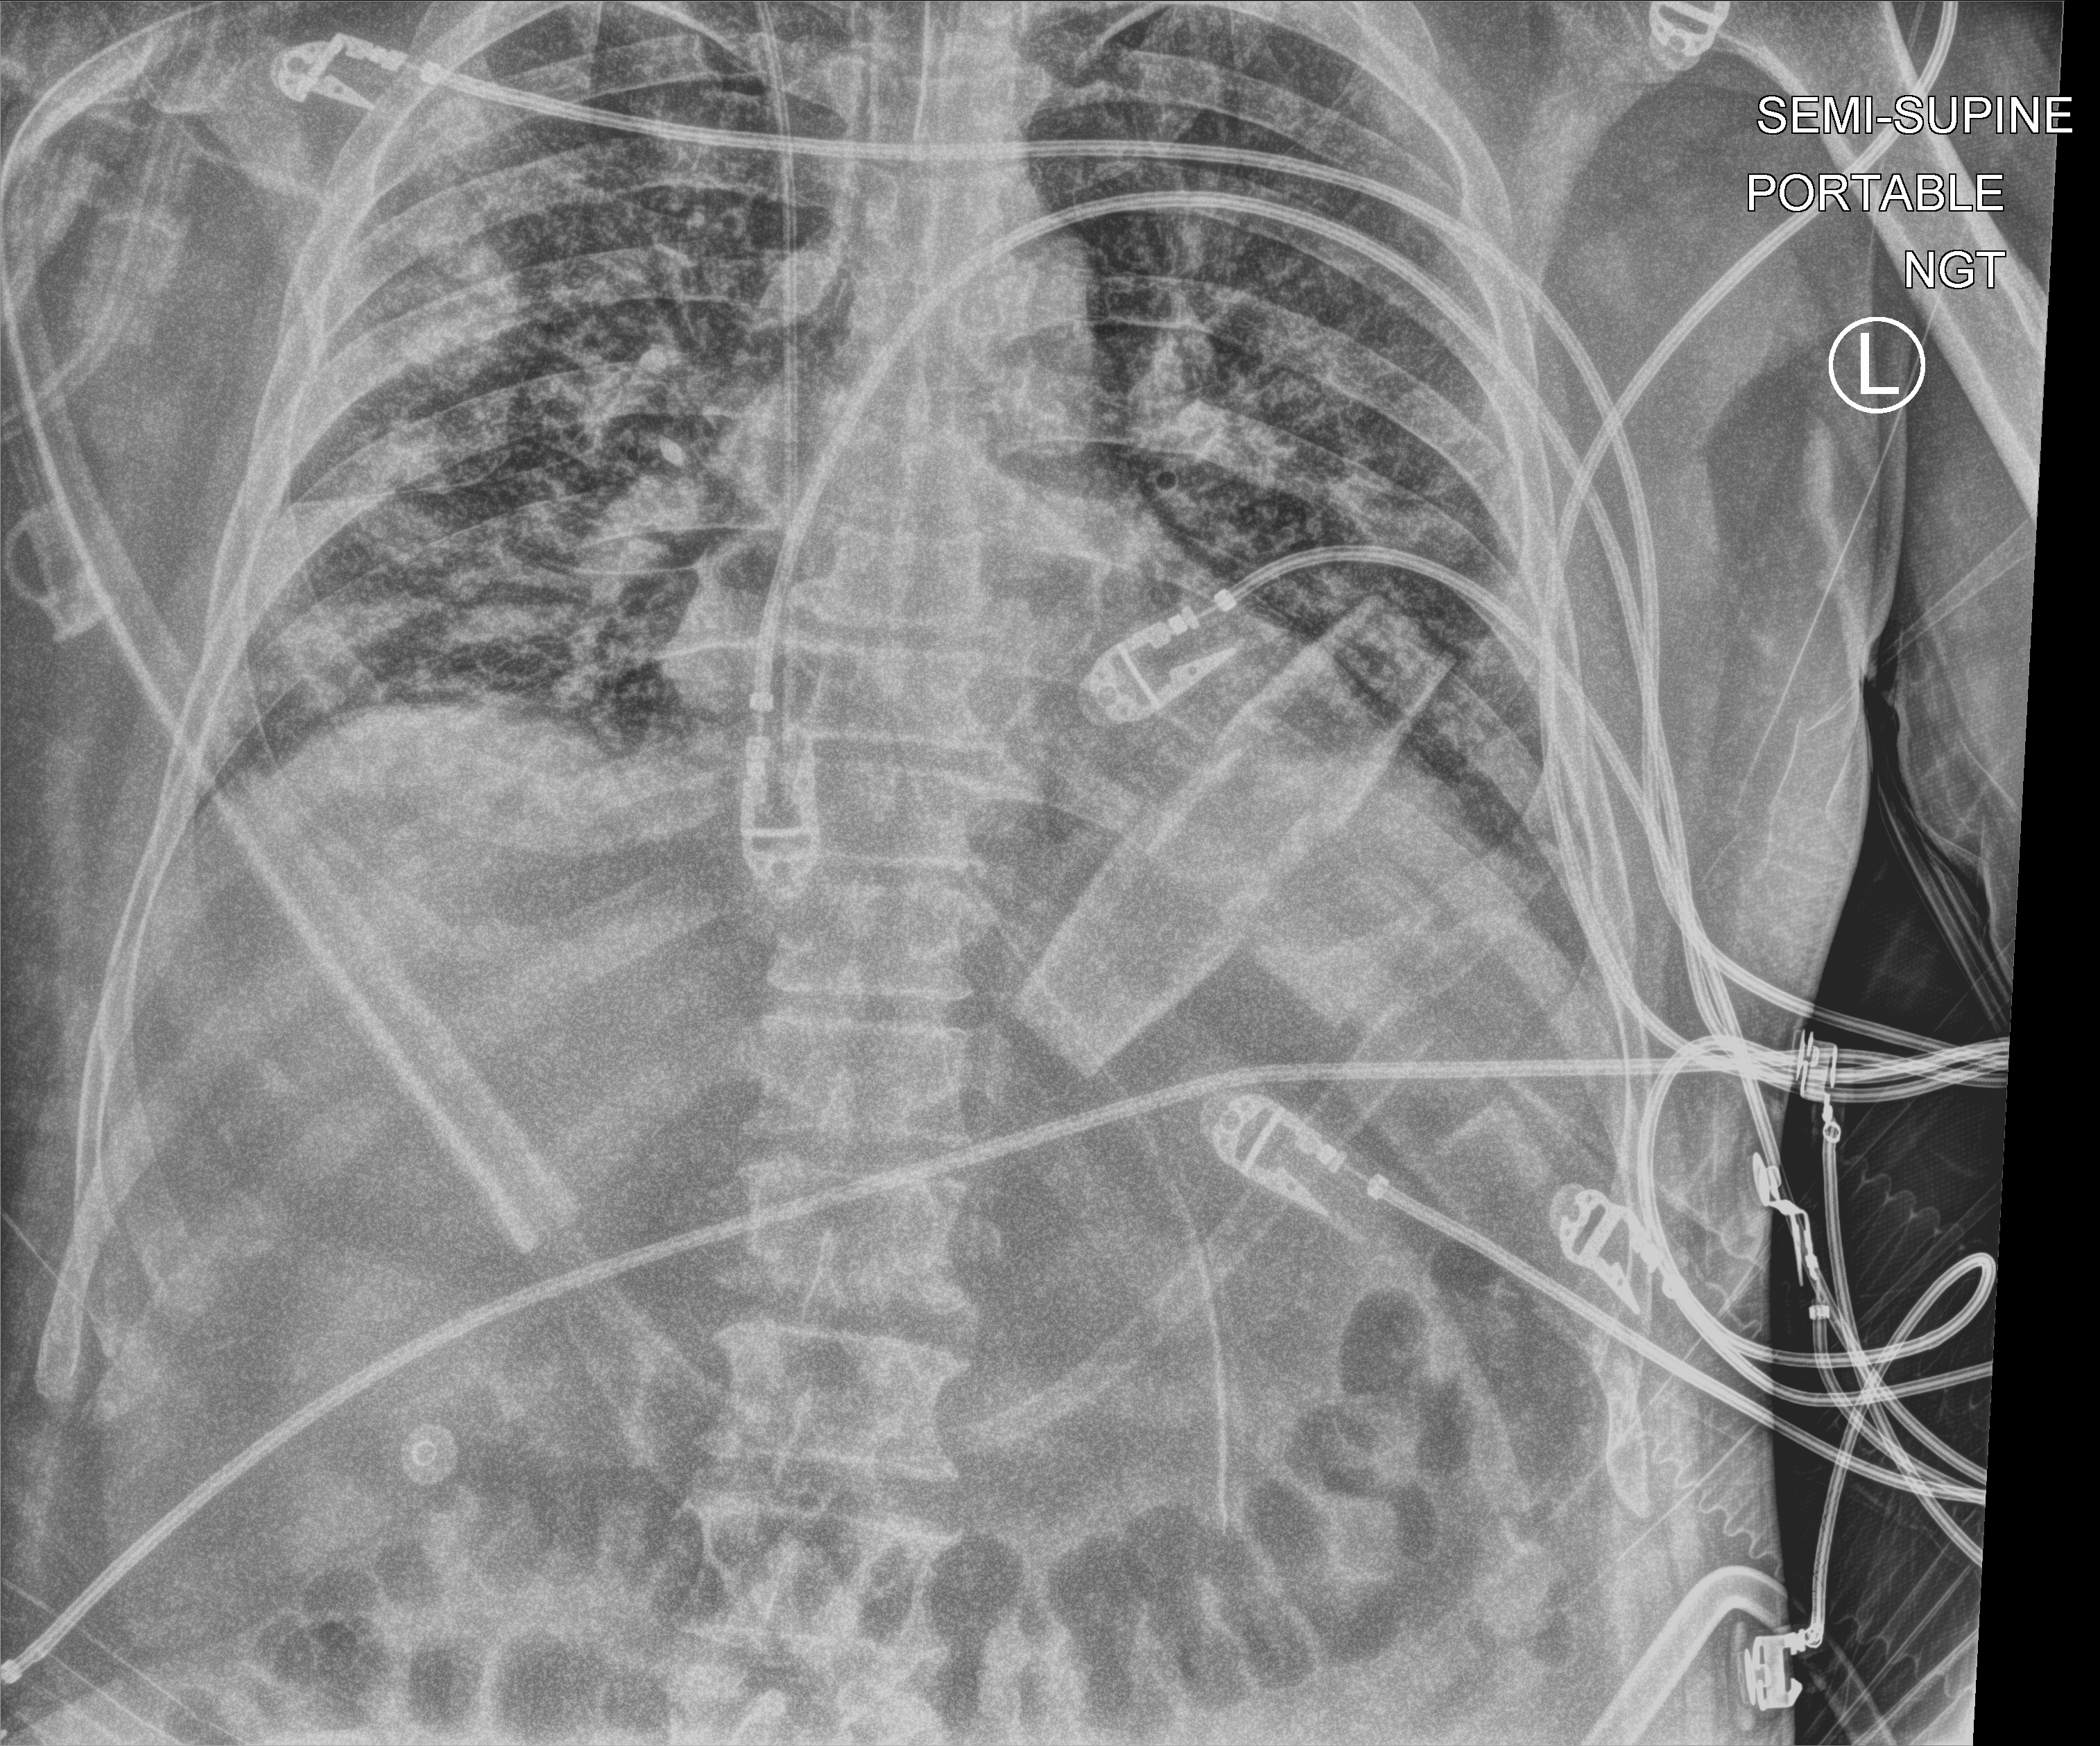
Chest X-ray (portable), anteroposterior (AP) projection. Male patient hospitalised with COVID-19, age 18–59 years.
Admission-level facts for this patient (not findings on this image; timing relative to this image not recorded): length of hospital stay: 11 days; mechanically ventilated during this hospital stay: yes.